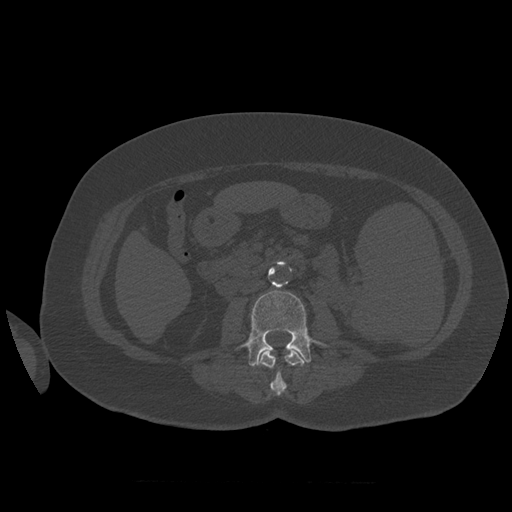
CT including the spine, one axial slice. Slice 237 of 399 in the series (ordered by position). Reconstruction kernel STANDARD. 120 kVp. Bone window (W 1800 / L 400 HU). 1.25 mm slice thickness. 512 × 512 image matrix. Patient age 81 years. Case-level facts recorded for this patient, not image findings: primary cancer: renal; vertebrae with lytic lesions (as recorded): L1.
Annotated regions visible in this slice (semi-automatic segmentation, software-assisted and operator-edited):
- L2 vertebra: bounding box <258,349,308,396> (left, top, right, bottom; pixels)
- L3 vertebra: <241,291,327,368>